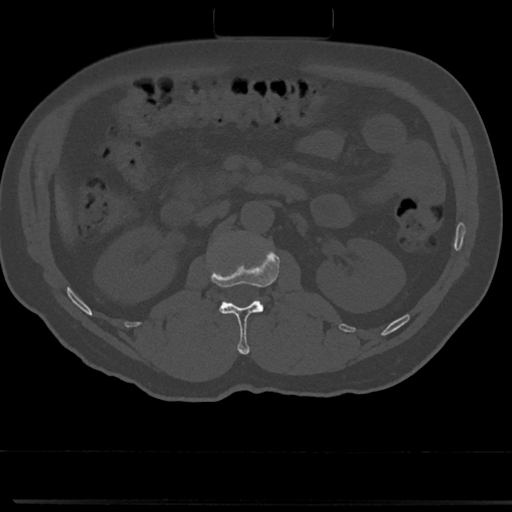
CT including the spine, one axial slice. Position 63 of 817 along the scan axis. Reconstruction kernel Br40s/3. Bone window (W 1800 / L 400 HU). 512 × 512 image matrix, field of view 355 × 355 mm. Male patient, age 61 years. From the clinical record (not read from this slice): primary cancer: prostate.
Structures marked on this image (semi-automatically segmented with operator editing):
- L1 vertebra: bounding box [x1, y1, x2, y2] px = [208, 240, 279, 354]